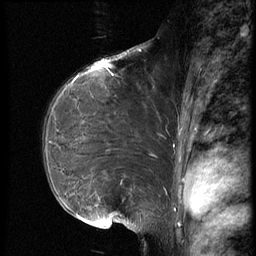
Breast MRI (dynamic contrast-enhanced), one sagittal slice. Dynamic contrast-enhanced series, image 2 of 3 at this slice position (ordered by acquisition). 1.5 T. TE 4.2 ms, TR 8.9 ms. 2.5 mm slice thickness. 256 × 256 image matrix, field of view 200 × 200 mm. Patient: female, 39 years. From the clinical record (not read from this slice): setting: breast cancer imaged before/during neoadjuvant chemotherapy; receptor status: HER2-positive.
Outlined on this slice (semi-automatically segmented with operator editing):
- analysis volume of interest (the breast-tissue region the enhancement analysis was run in; not a lesion): box from (x=40, y=75) to (x=173, y=218) px
- tumour enhancement mask (voxels above the 140 % enhancement threshold inside the analysis volume of interest): (x=111, y=75)–(x=114, y=77)